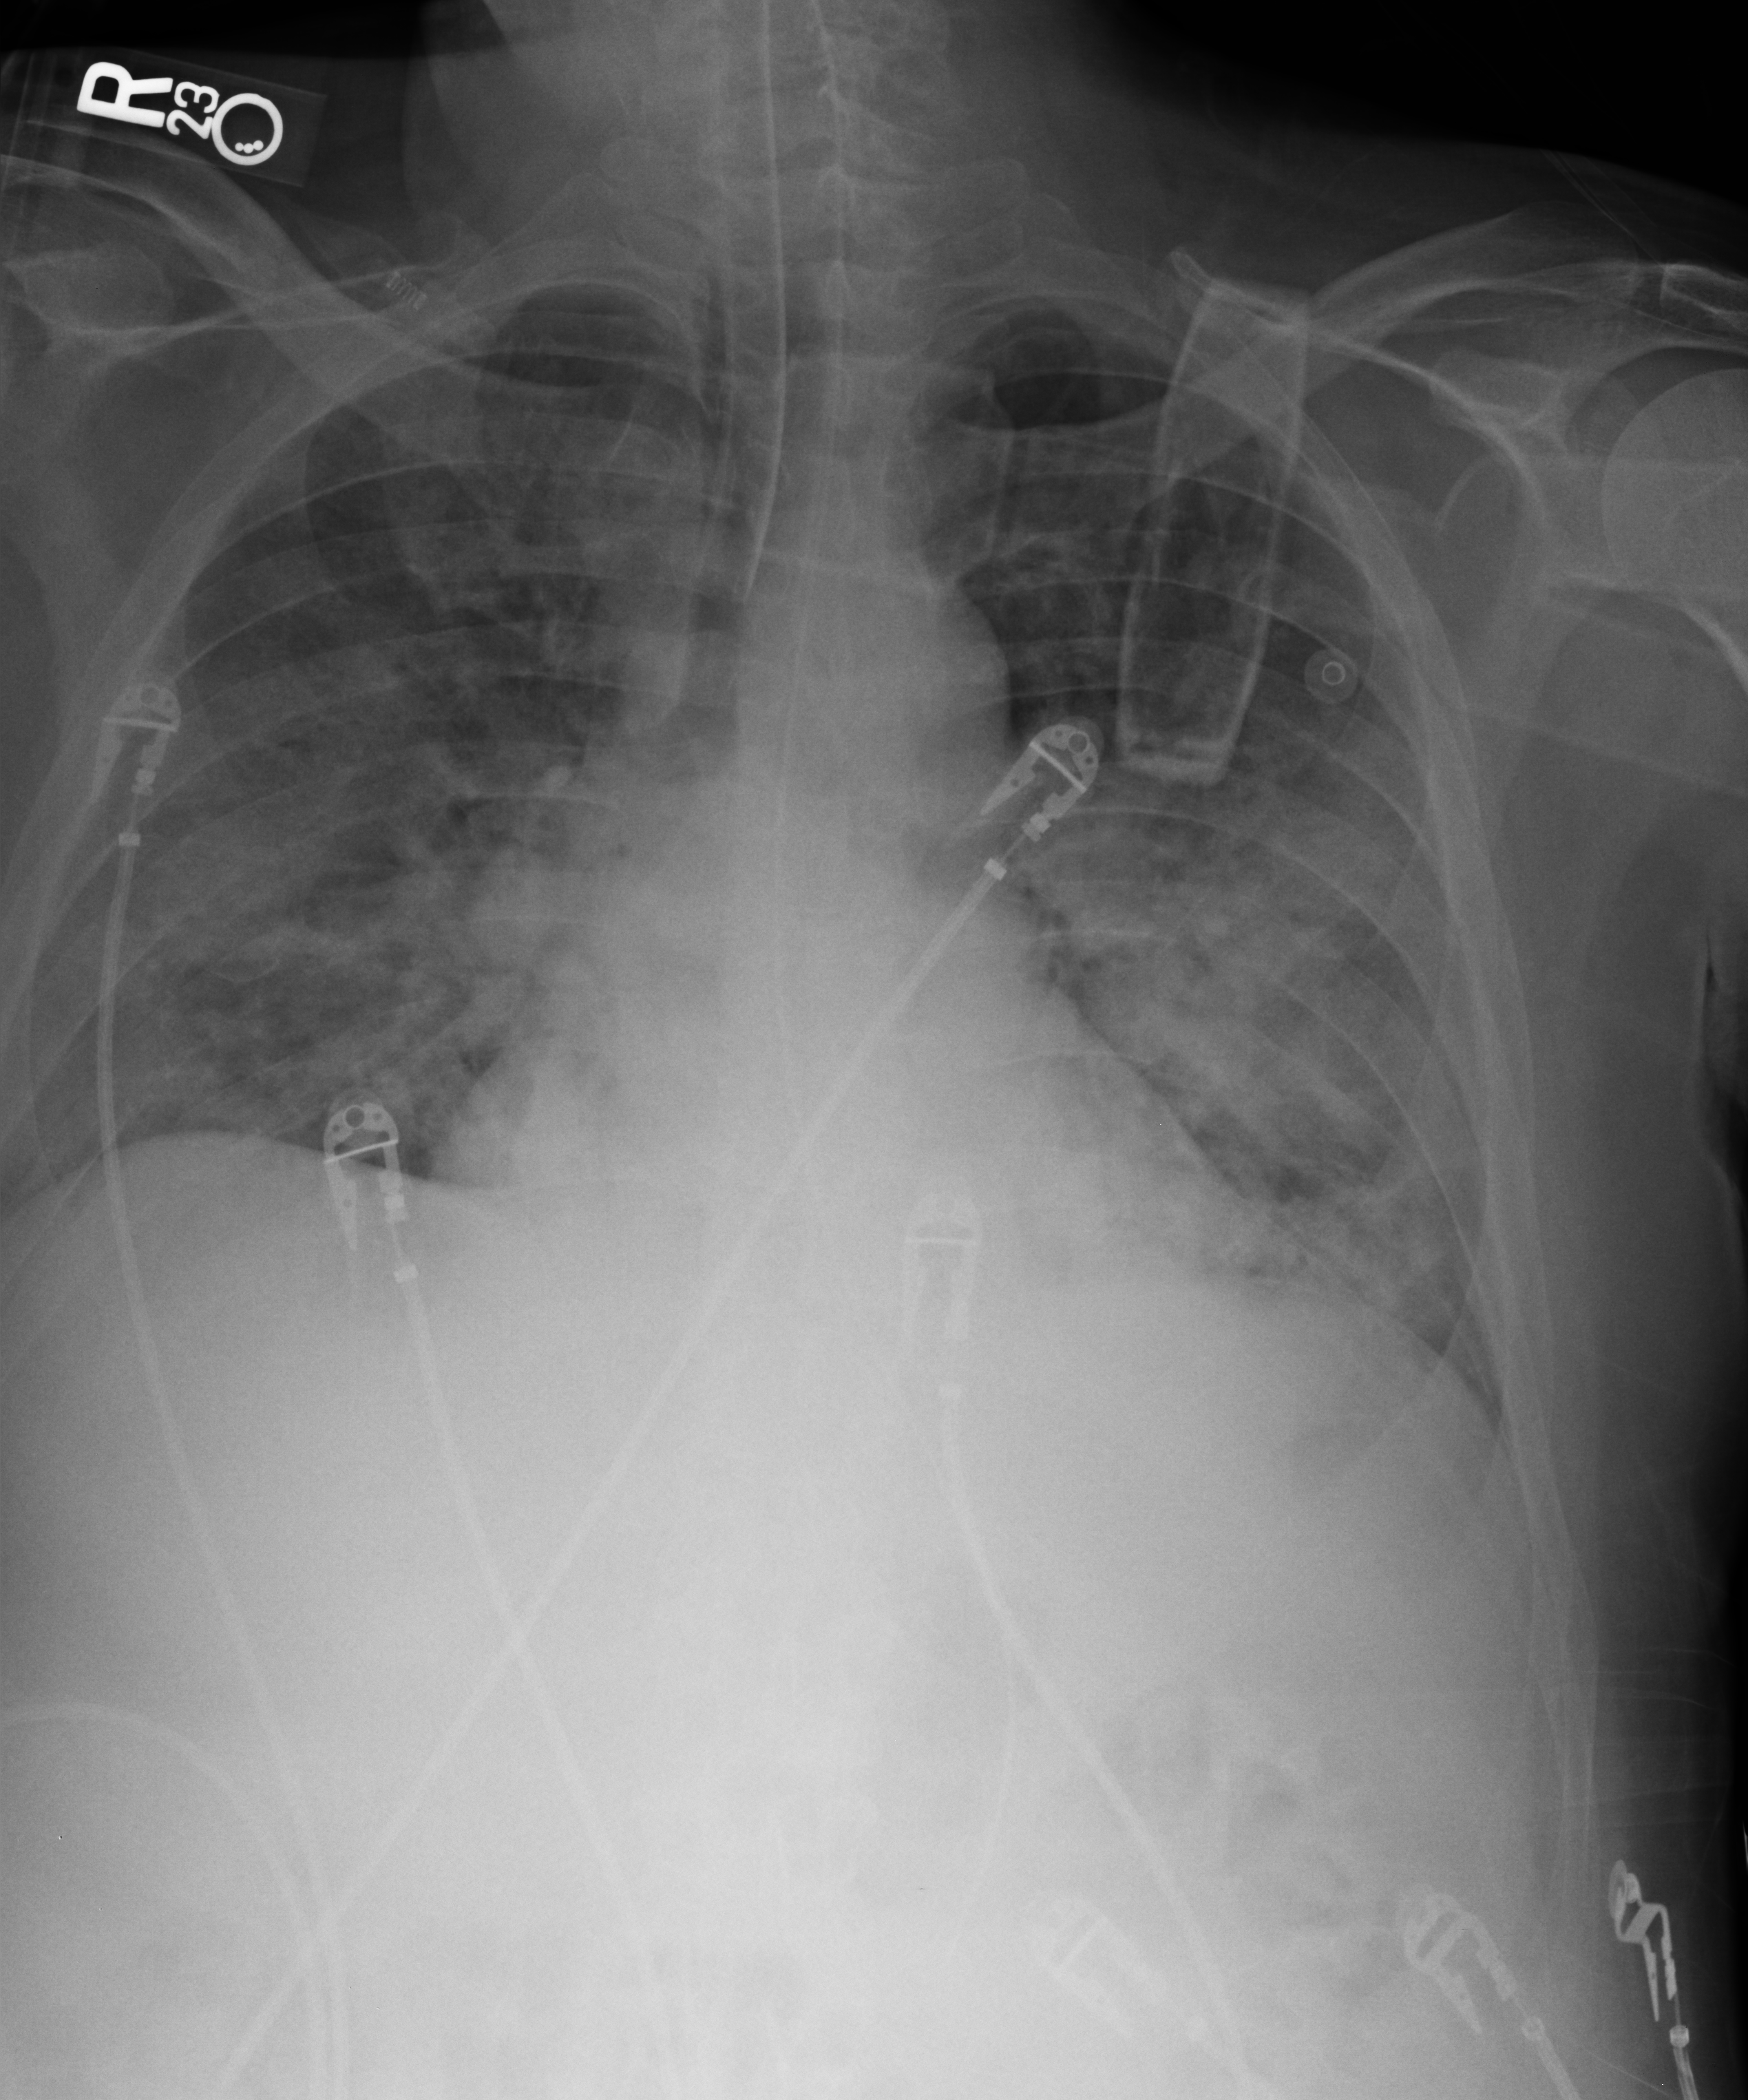
Chest X-ray (portable); anteroposterior (AP) projection. Male patient hospitalised with COVID-19, age 18–59 years.
Admission-level facts for this patient (not findings on this image; timing relative to this image not recorded):
- length of hospital stay: 20 days
- smoking status (admission record): never
- admitted to intensive care during this hospital stay: yes